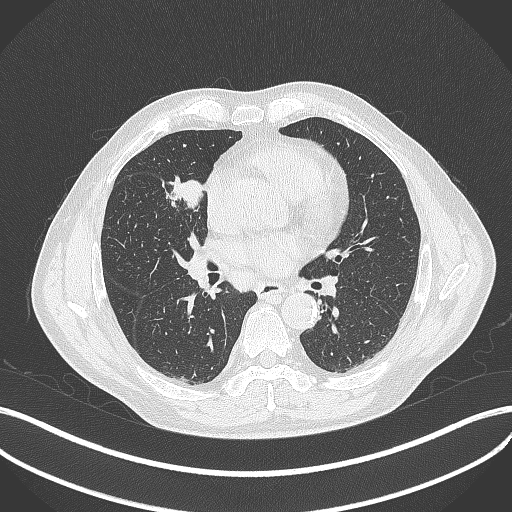
Chest CT, one axial slice; slice 201 of 429 in the series (ordered by position); 120 kVp; lung window (W 1500 / L -600 HU); 512 × 512 image matrix, field of view 400 × 400 mm. Male patient, age 61 years. From the clinical record (not read from this slice): clinical TNM (as recorded): T2b N1 M0.
Outlined on this slice (rectangle marked by the reading radiologist):
- lung tumour (recorded histology: squamous cell carcinoma): bounding box [x1, y1, x2, y2] px = [167, 176, 206, 211]